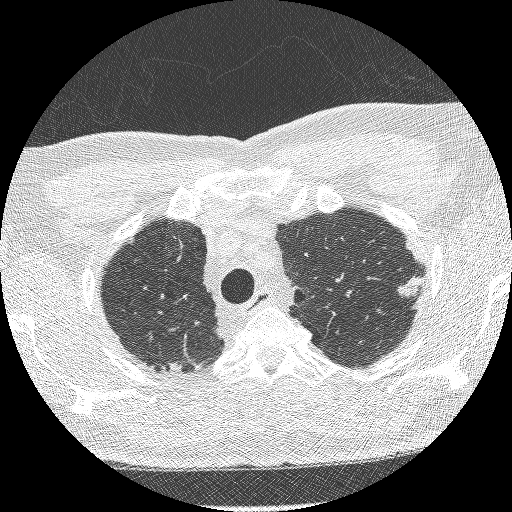
Axial slice from a low-dose chest CT screening exam. Third annual screen. Lung window (W 1500 / L -600 HU). 1.25 mm slice thickness. Lung (sharp) reconstruction kernel (BONE). 120 kVp. Slice 237 of 275 in the series. 512 × 512 image matrix. Male participant, aged 66 years at enrolment. Current smoker at enrolment.
• Expert reader's lesion annotation, bounding box <390,269,433,310> (left, top, right, bottom; pixels).
• Reader record for this screening exam (exam-level; its link to the box is not recorded): non-calcified nodule or mass ≥4 mm, left lower lobe, 15 × 9 mm, spiculated (stellate) margins, soft tissue attenuation, pre-existing on the prior screen: yes; interval growth: yes.
• Official screen result: positive, other.
• Lung cancer was diagnosed 225 days after this screen: adenocarcinoma, NOS, left upper lobe, poorly differentiated (G3), stage IB (AJCC 6th edition), 16 mm at pathology.